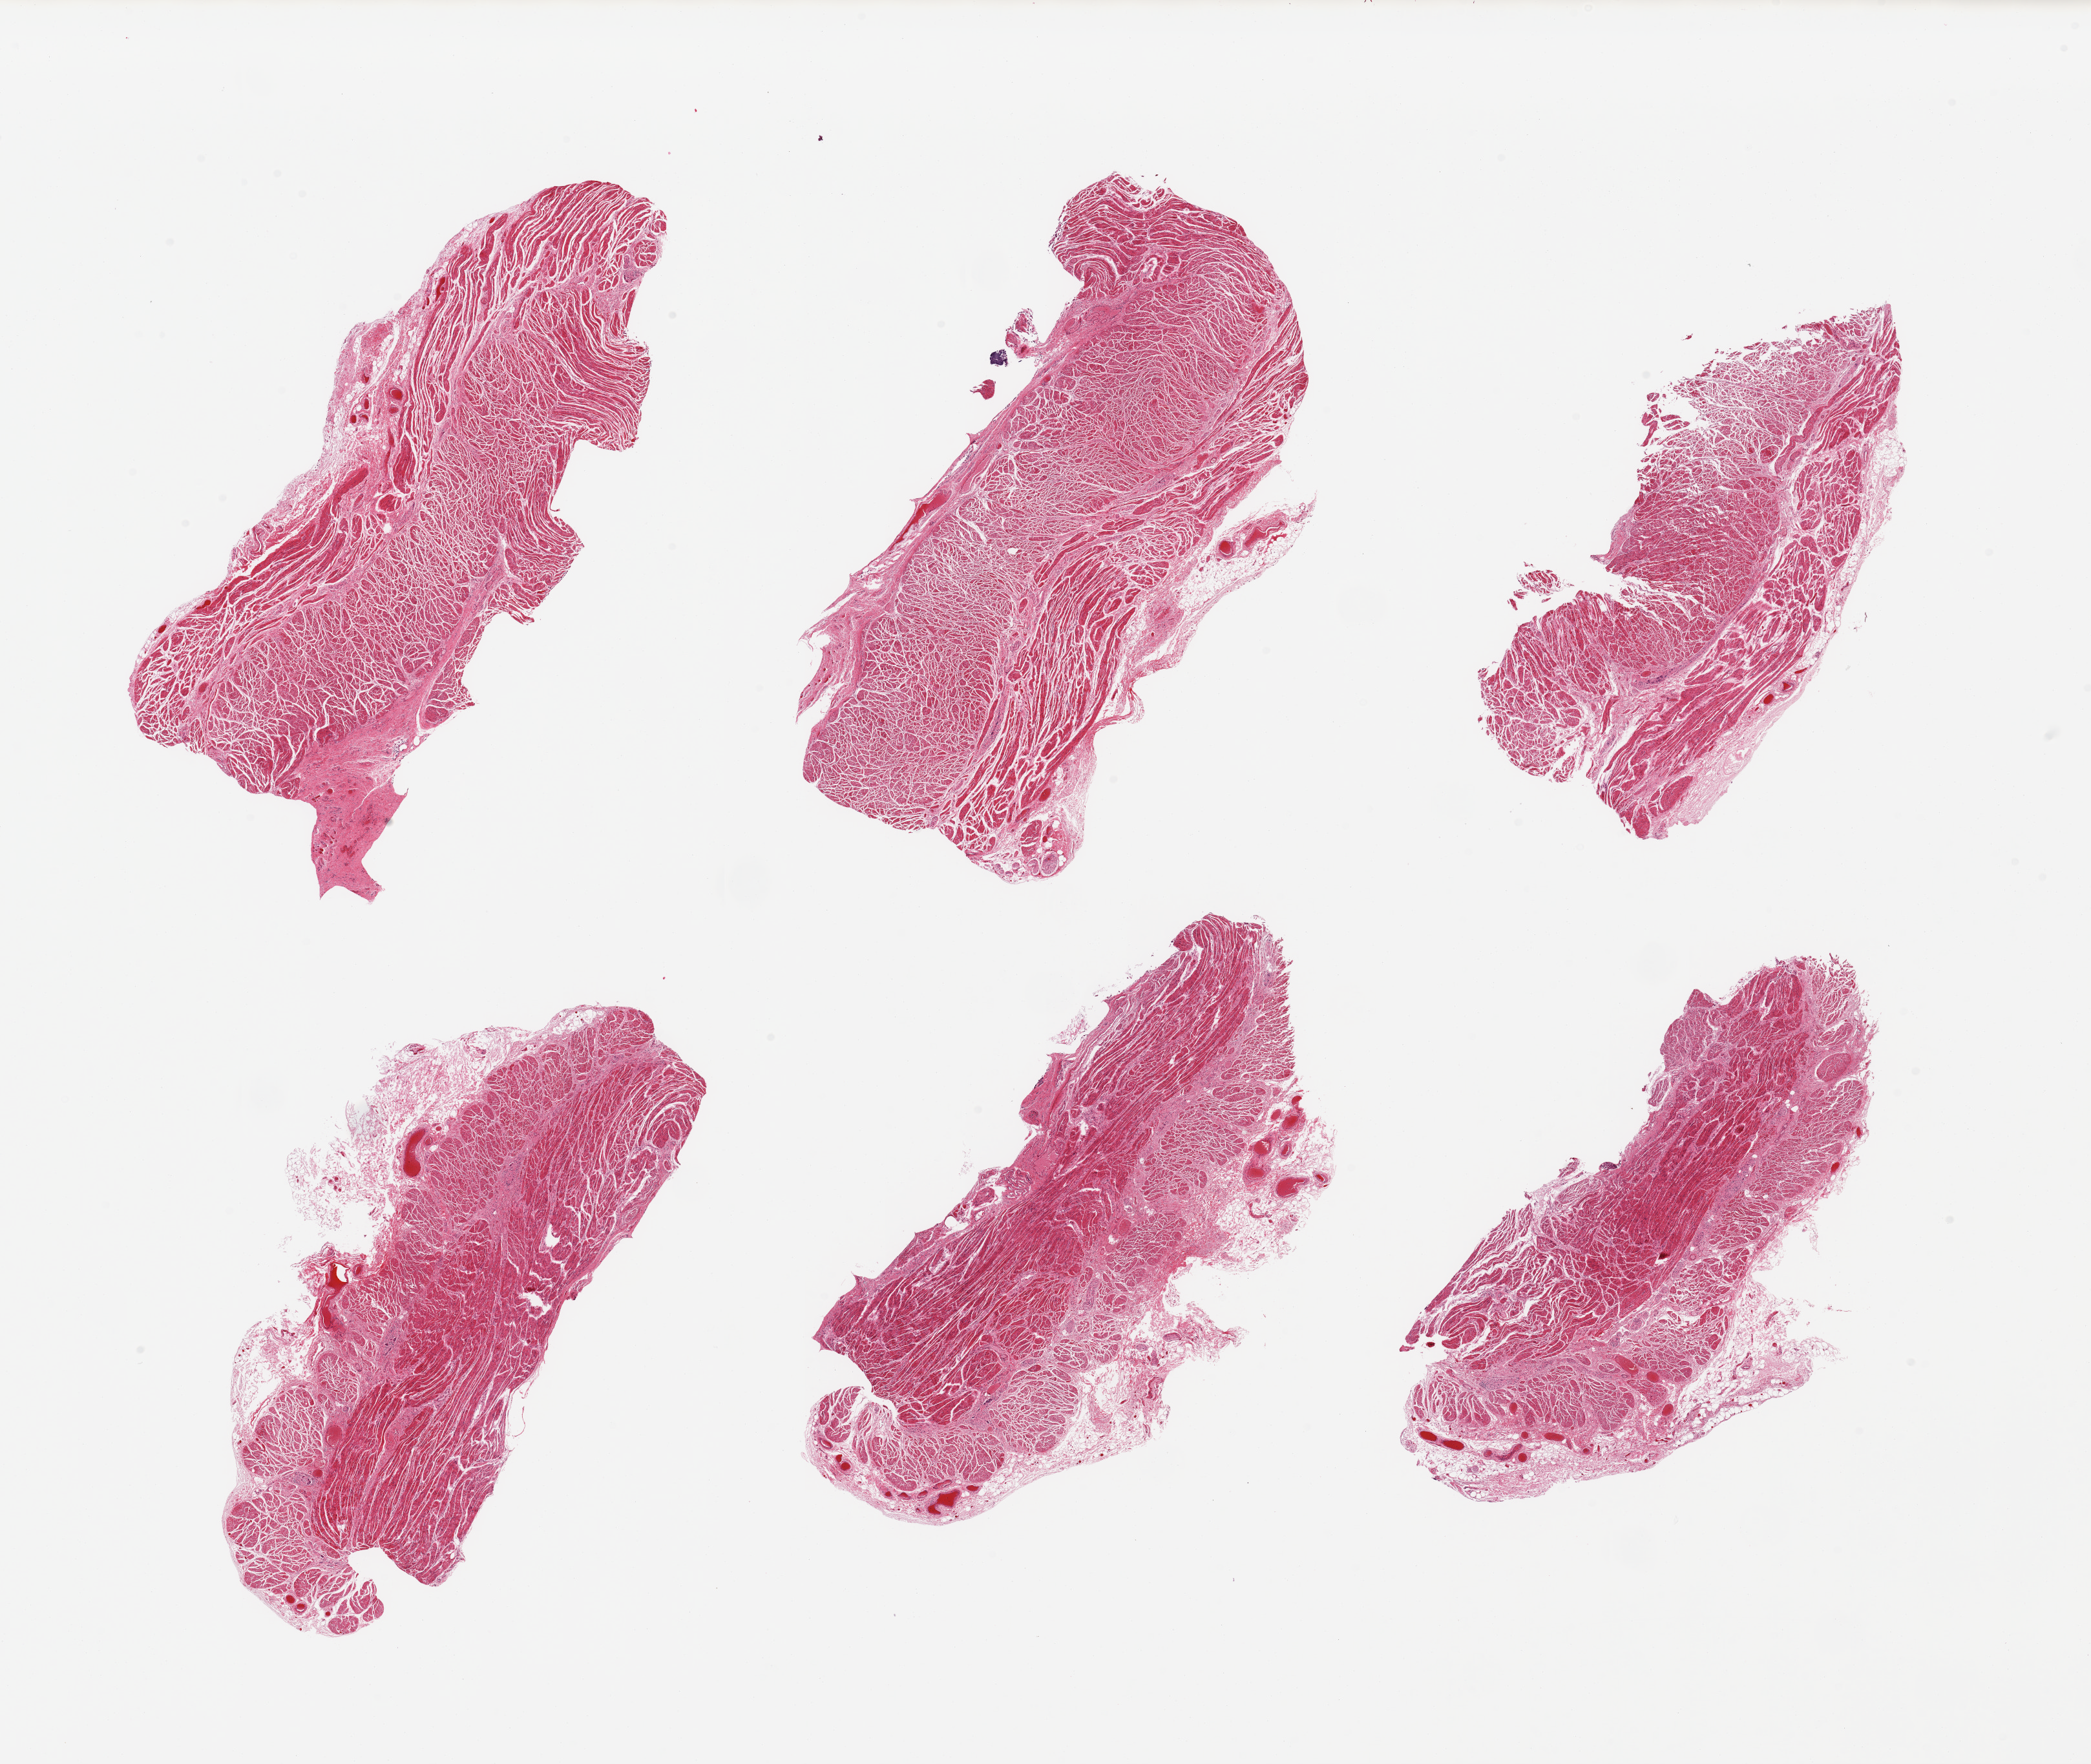
Whole-slide image, H&E stain, brightfield, low-resolution overview of the scanned area, about 25.6 x 21.6 mm. PAXgene-fixed, paraffin-embedded tissue. Section of gastroesophageal junction (target tissue). Donor tissue sample. Donor sex: female.
Reviewer comment on this tissue sample: 6 pieces; 5% fibrofatty content.